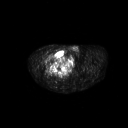
FDG PET of an extremity soft-tissue mass (from a PET/CT study), one axial slice. Slice 274 of 311 in the series (ordered by position). 128 × 128 image matrix, field of view 700 × 700 mm. Male patient, age 50 years. From the clinical record (not read from this slice): histological type: undifferentiated - pleiomorphic; grade: high; site of the primary tumour: right thigh.
Annotated regions visible in this slice (expert contour drawn on MRI and transferred to this co-registered scan by the dataset authors):
- gross tumour volume including surrounding oedema: bounding box [x1, y1, x2, y2] px = [47, 49, 66, 68]
- gross tumour volume (mass): [47, 49, 66, 68]